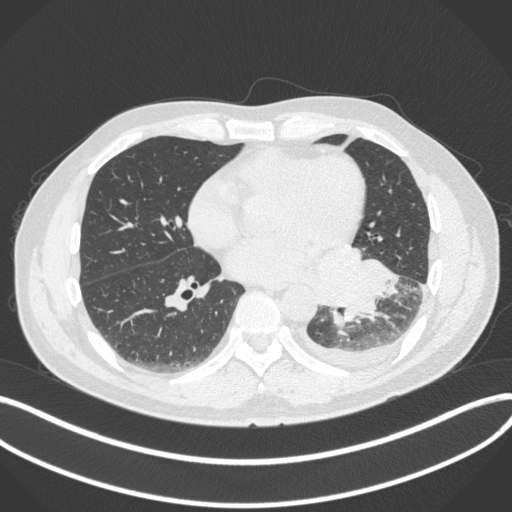
Chest CT, one axial slice; slice 151 of 350 in the series (ordered by position); lung window (W 1500 / L -600 HU); 512 × 512 image matrix. Patient: male, 58 years. From the clinical record (not read from this slice): clinical TNM (as recorded): T3 N1 M1b; histopathological grade: G3.
Annotated regions visible in this slice (rectangle marked by the reading radiologist):
- lung tumour (recorded histology: small cell carcinoma): bounding box [x1, y1, x2, y2] px = [342, 254, 400, 330]